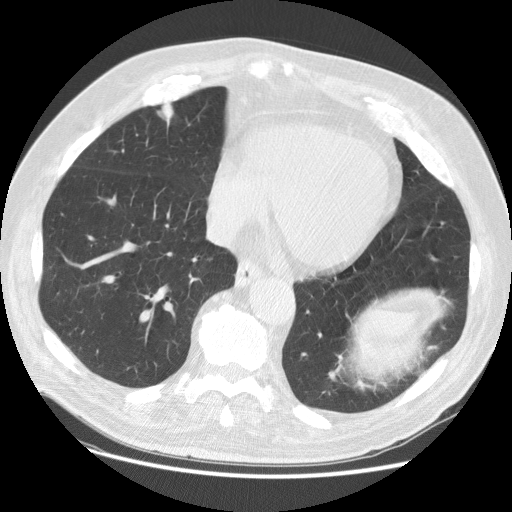
Axial slice from a low-dose chest CT screening exam; baseline annual screen; lung window (W 1500 / L -600 HU); standard (soft-tissue) reconstruction kernel (STANDARD). Male, age 74 years at enrolment.
Expert-annotated lung lesion, box from (x=149, y=93) to (x=187, y=140) px. Screening reader's record for this exam (one nodule recorded; not confirmed to be the boxed lesion): non-calcified nodule or mass ≥4 mm, right middle lobe, 24 × 24 mm, spiculated (stellate) margins, soft tissue attenuation. Official screen result: positive, change unspecified: nodule(s) >= 4 mm or enlarging nodule(s), mass(es), or other non-specific abnormalities suspicious for lung cancer. Later outcome: lung cancer diagnosed 296 days after this screen — papillary adenocarcinoma, NOS, right middle lobe, well differentiated (G1), stage IA (AJCC 6th edition), 20 mm at pathology.